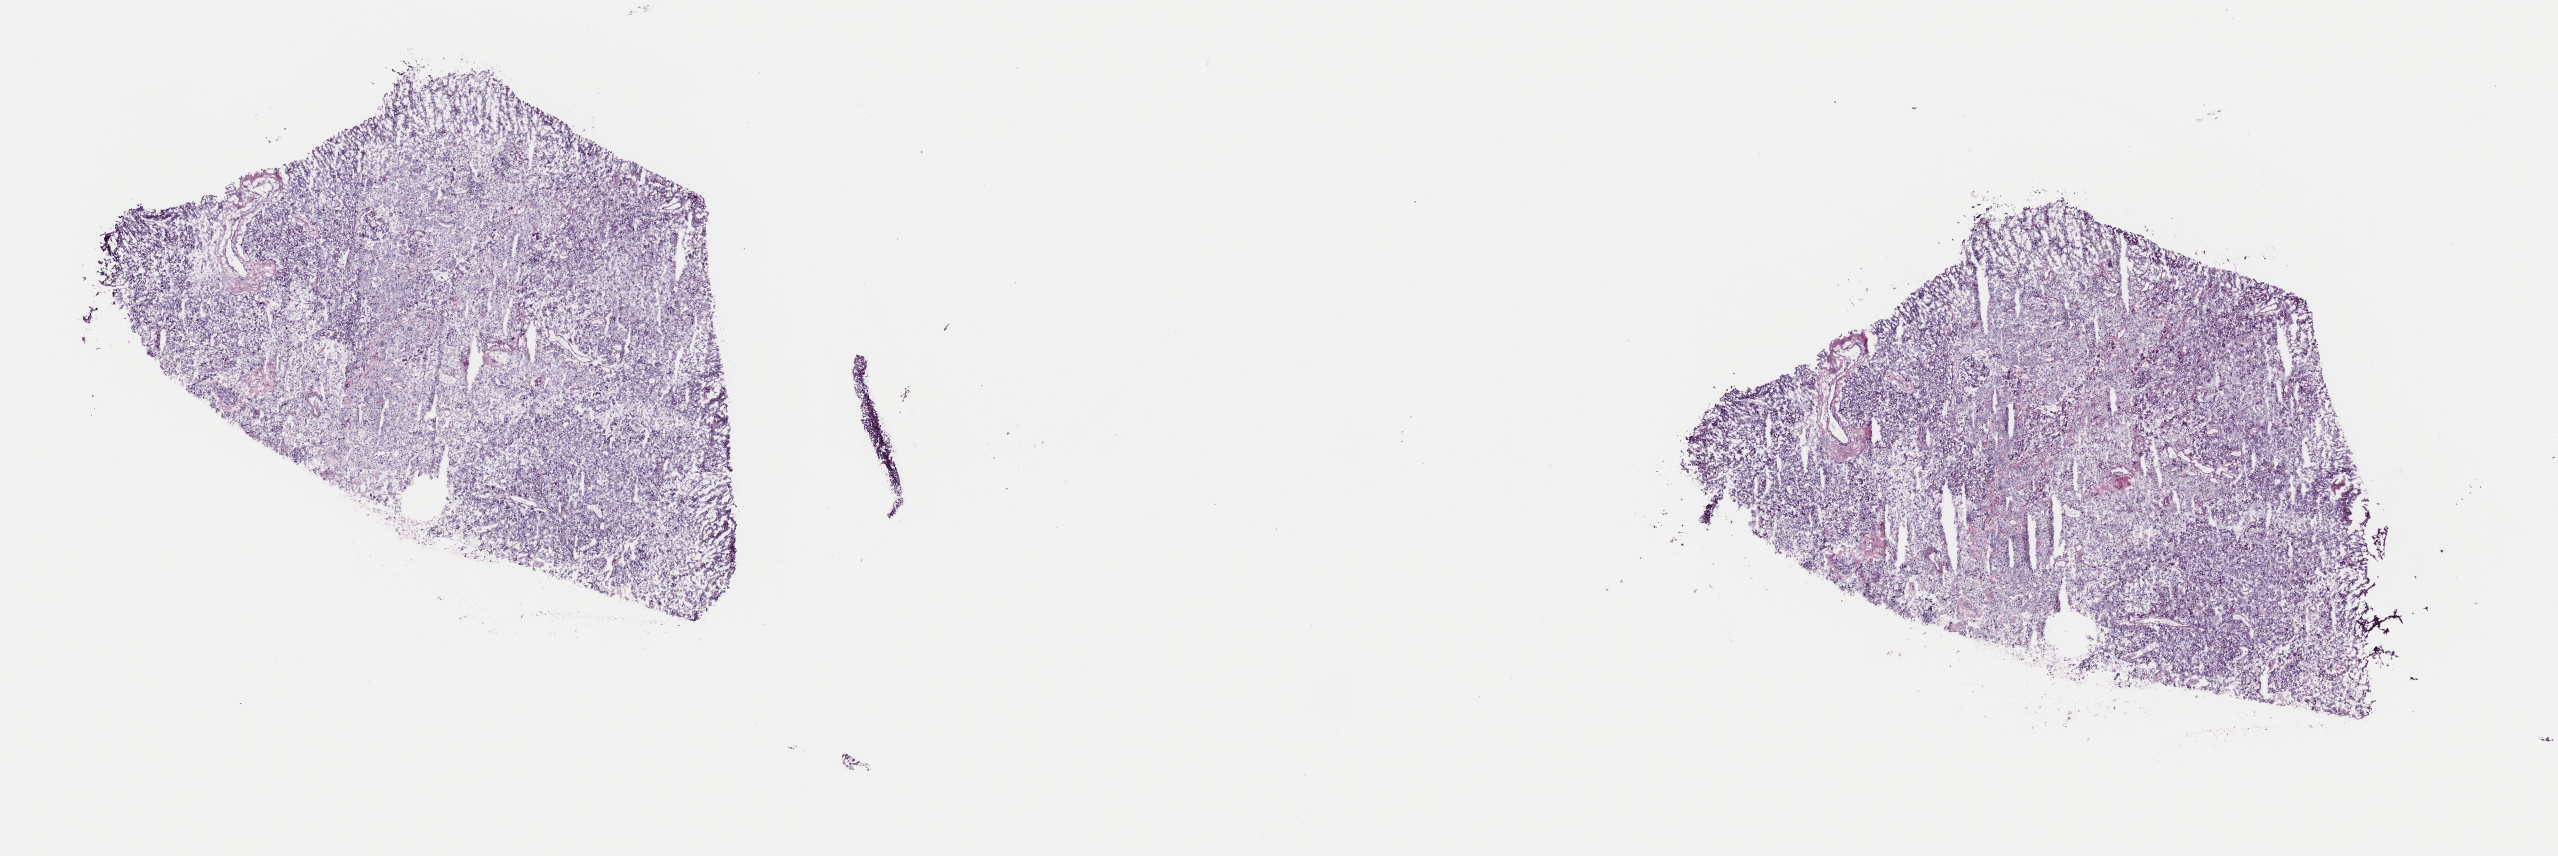
Digitized H&E-stained tissue section (whole slide) — whole scanned area (about 20.2 x 6.8 mm, from a 40x scan) shown as a low-resolution overview. Frozen section. Sample: primary tumour, brain. Patient: male, age at initial diagnosis 68 years. Composition of this section per pathologist review: tumour cells 30%, tumour nuclei 70%, normal cells 10%, stromal cells 15%, necrosis 45%. Infiltration values recorded for this section: lymphocyte infiltration 5%, monocyte infiltration 0%, neutrophil infiltration 0%.
Histologic diagnosis: Glioblastoma.